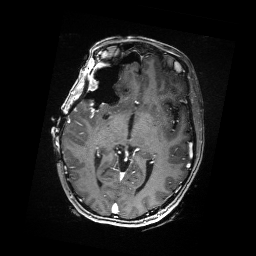
Brain MRI from a brain-tumour surgery series, one axial slice; position 97 of 176 along the scan axis; T1-weighted post-contrast; 1 mm slice thickness; 256 × 256 image matrix. From the clinical record (not read from this slice): histopathology: Metastatic Carcinoma from Breast primary; tumour location: Right Frontal.
Outlined on this slice (outlined manually by an expert reader):
- residual tumour: bounding box <97,69,108,88> (left, top, right, bottom; pixels)